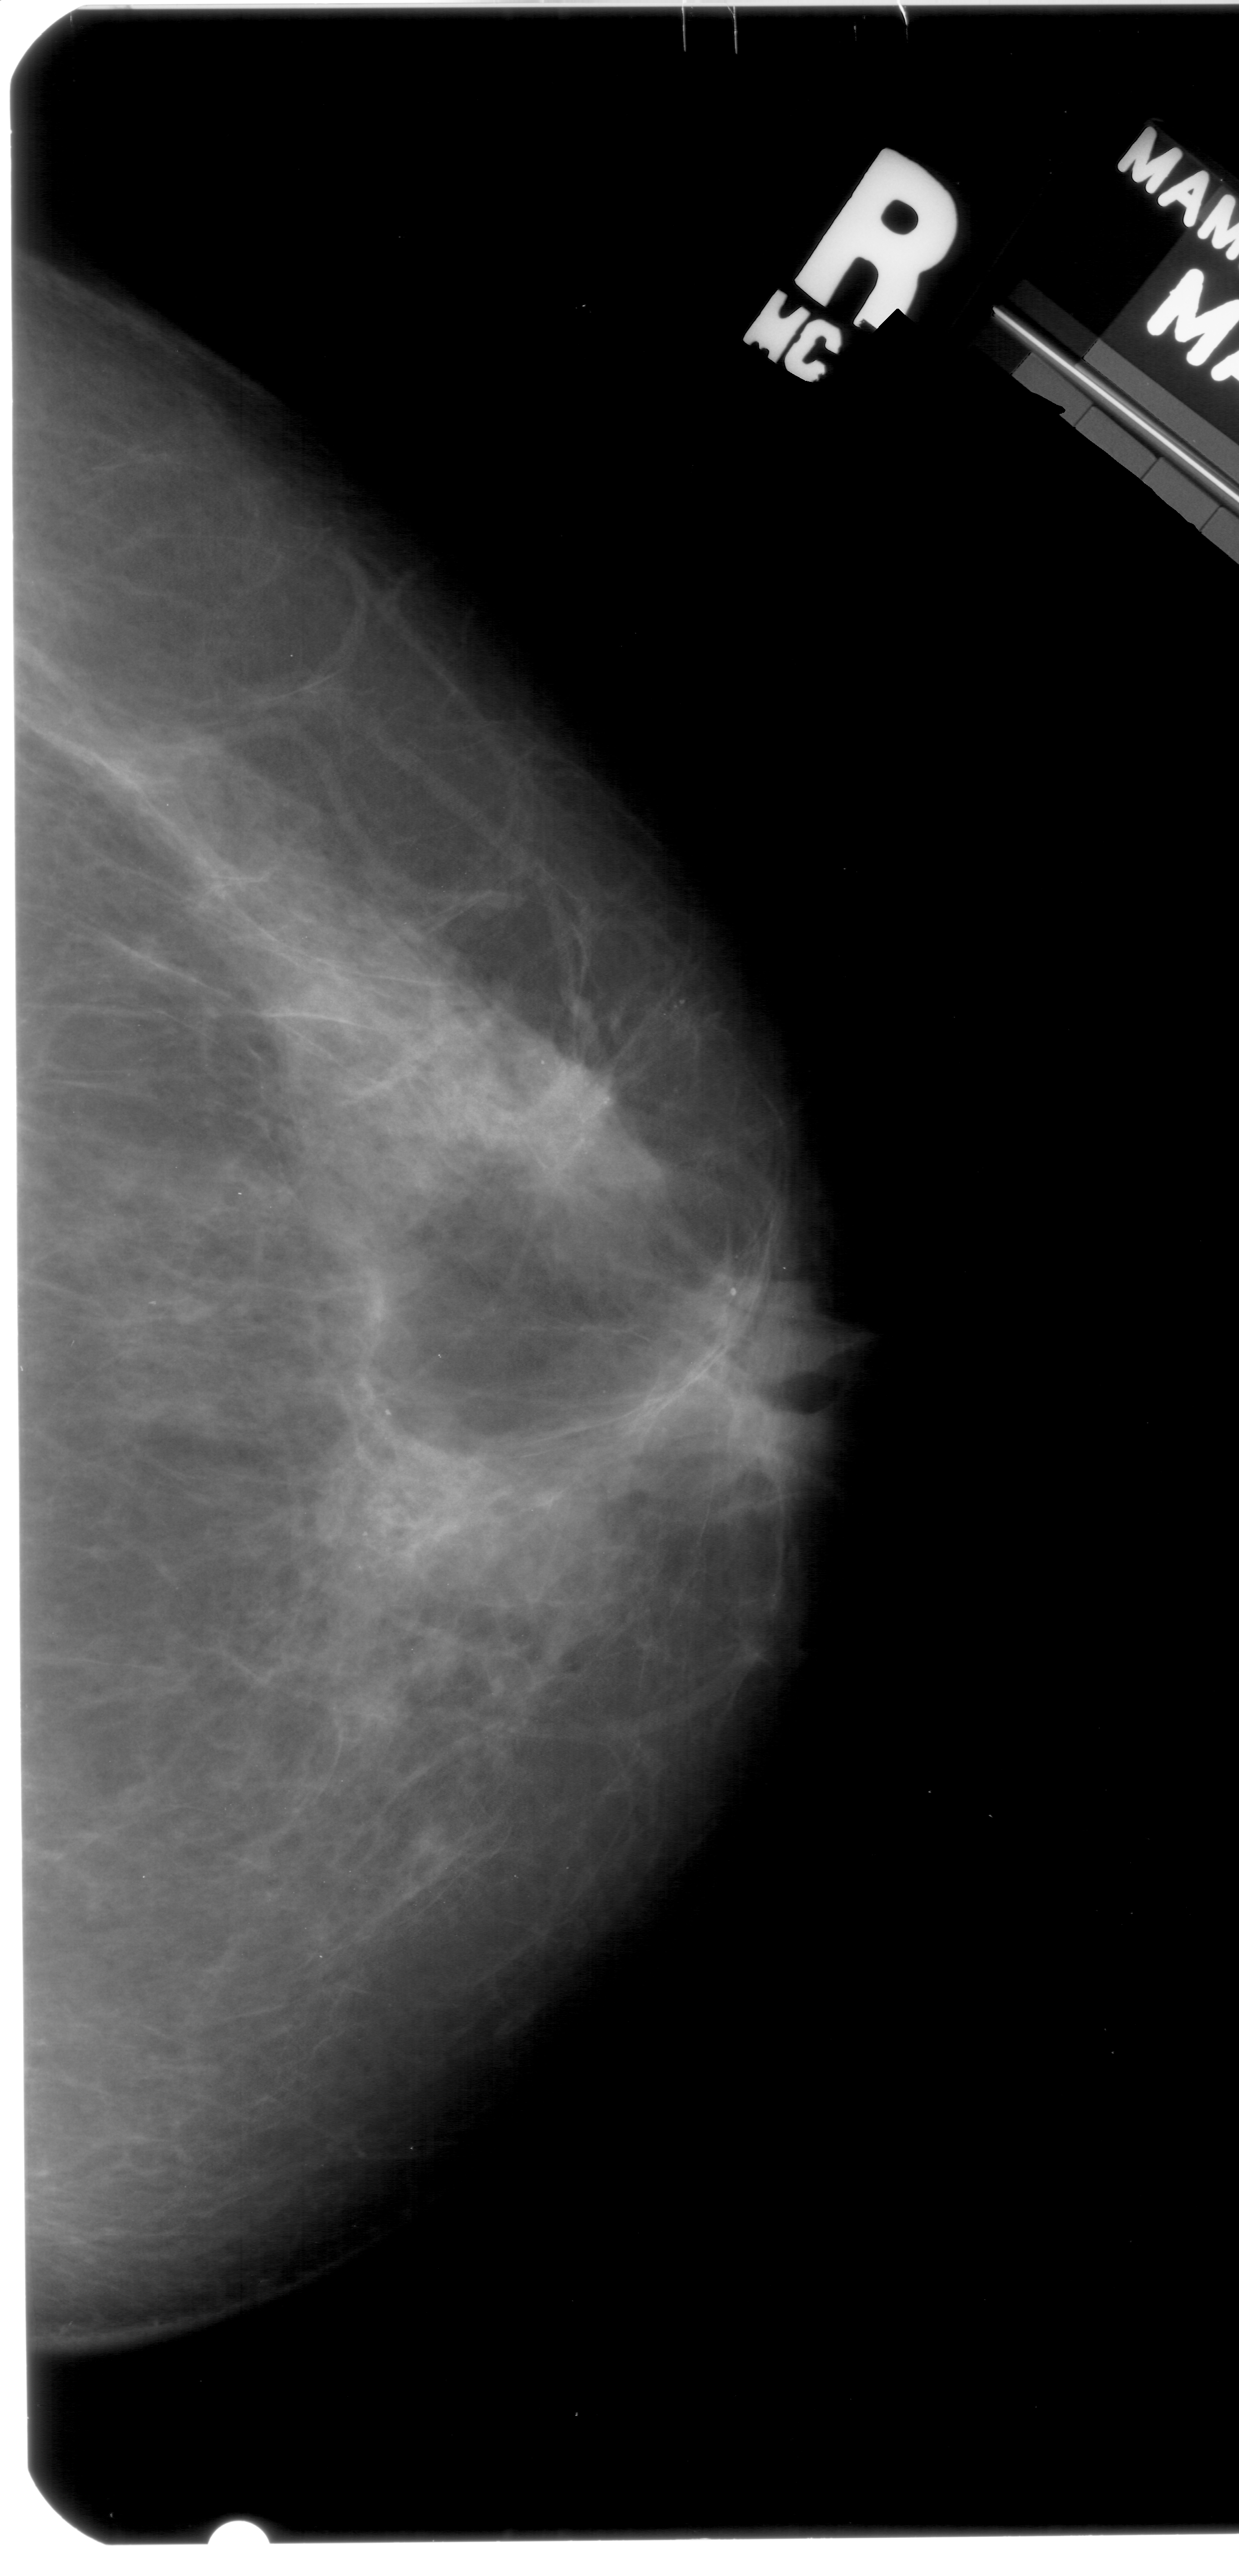
Scanned film-screen mammogram. Right breast. CC view. Breast composition: extremely dense (BI-RADS density category 4 of 4). 1239 × 2576 image matrix.
Expert-marked regions of interest on this film, with their recorded descriptors:
- calcifications, morphology pleomorphic, distribution clustered; BI-RADS assessment category 4; pathology (as recorded): malignant: bounding box [x1, y1, x2, y2] px = [482, 989, 703, 1233]